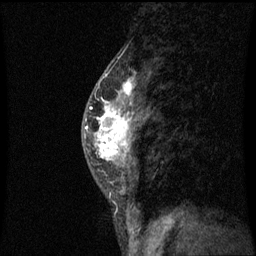
Breast MRI (dynamic contrast-enhanced), one sagittal slice; position 29 of 60 along the scan axis; dynamic contrast-enhanced series, image 2 of 3 at this slice position (ordered by acquisition); 1.5 T; TE 4.2 ms, TR 8.9 ms; 256 × 256 image matrix, field of view 200 × 200 mm. Patient: female, 50 years. Case-level facts recorded for this patient, not image findings: setting: breast cancer imaged before/during neoadjuvant chemotherapy; receptor status: triple-negative.
Structures marked on this image (semi-automatically segmented with operator editing):
- analysis volume of interest (the breast-tissue region the enhancement analysis was run in; not a lesion): box from (x=84, y=80) to (x=143, y=171) px
- tumour enhancement mask (voxels above the 70 % enhancement threshold inside the analysis volume of interest): (x=86, y=80)–(x=135, y=161)